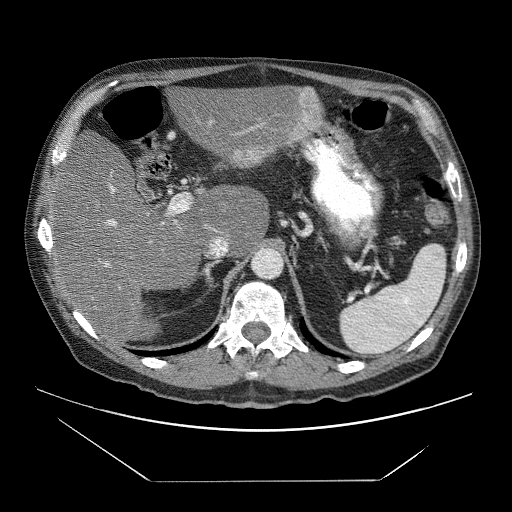
Contrast-enhanced abdominal CT (liver protocol), one axial slice; slice 40 of 83 in the series (ordered by position); reconstruction kernel STANDARD; 120 kVp; soft-tissue window (W 400 / L 40 HU); 2.5 mm slice thickness; 512 × 512 image matrix, field of view 420 × 420 mm. From the clinical record (not read from this slice): diagnosis: hepatocellular carcinoma (patient treated with transarterial chemoembolisation; whether this scan precedes or follows treatment is not stated here); TNM stage (as recorded): Stage-IVB; Child-Pugh class: B; tumour nodularity: uninodular.
Annotated regions visible in this slice (semi-automatic segmentation, software-assisted and operator-edited):
- liver parenchyma outside the tumour (the mass and vessels are separate outlines, so this box may not span the whole liver): bounding box [x1, y1, x2, y2] px = [48, 86, 322, 340]
- mass: [233, 91, 321, 167]
- liver vessels: [51, 127, 313, 267]